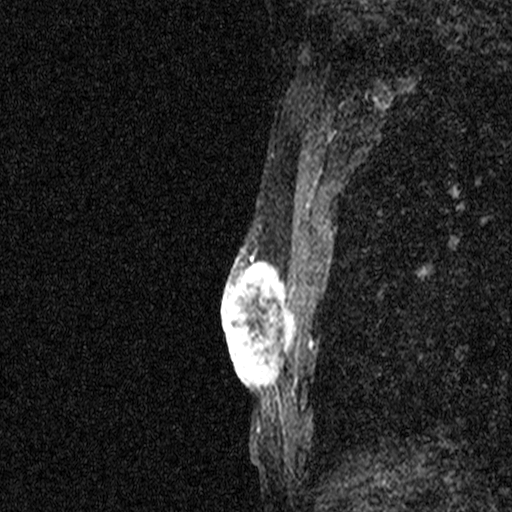
Breast MRI (dynamic contrast-enhanced), one sagittal slice. Dynamic contrast-enhanced study with each time point stored as its own series, time point 2 of 3 at this slice position (early post-contrast, ordered by acquisition time). 1.5 T. TE 4.5 ms, TR 11 ms. 2.05 mm slice thickness. 512 × 512 image matrix, field of view 200 × 200 mm. Patient: female, 44 years. From the clinical record (not read from this slice): setting: breast cancer imaged before/during neoadjuvant chemotherapy; receptor status: HR-positive, HER2-negative.
Annotated regions visible in this slice (semi-automatic segmentation, software-assisted and operator-edited):
- analysis volume of interest (the breast-tissue region the enhancement analysis was run in; not a lesion): bounding box <204,254,298,401> (left, top, right, bottom; pixels)
- tumour enhancement mask (voxels above the 90 % enhancement threshold inside the analysis volume of interest): <221,254,297,401>